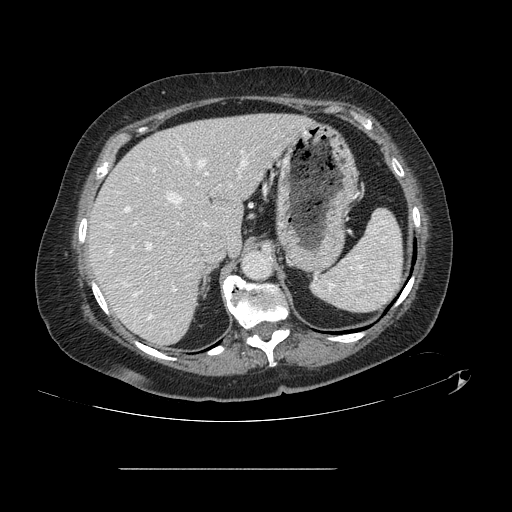
Contrast-enhanced abdominal CT, one axial slice; position 93 of 148 along the scan axis; intravenous contrast given; soft-tissue window (W 400 / L 40 HU); 512 × 512 image matrix, field of view 439 × 439 mm. Female patient, age 75 years. Case-level facts recorded for this patient, not image findings: diagnosis: colorectal cancer liver metastases, imaged before liver resection; multiple liver metastases: no.
Structures marked on this image (outlined manually by an expert reader):
- hepatic veins: bounding box [x1, y1, x2, y2] px = [135, 159, 245, 319]
- liver: [90, 115, 309, 345]
- planned liver remnant (the part of the liver to remain after resection): [90, 114, 308, 345]
- portal vein (with intrahepatic branches): [125, 150, 248, 291]